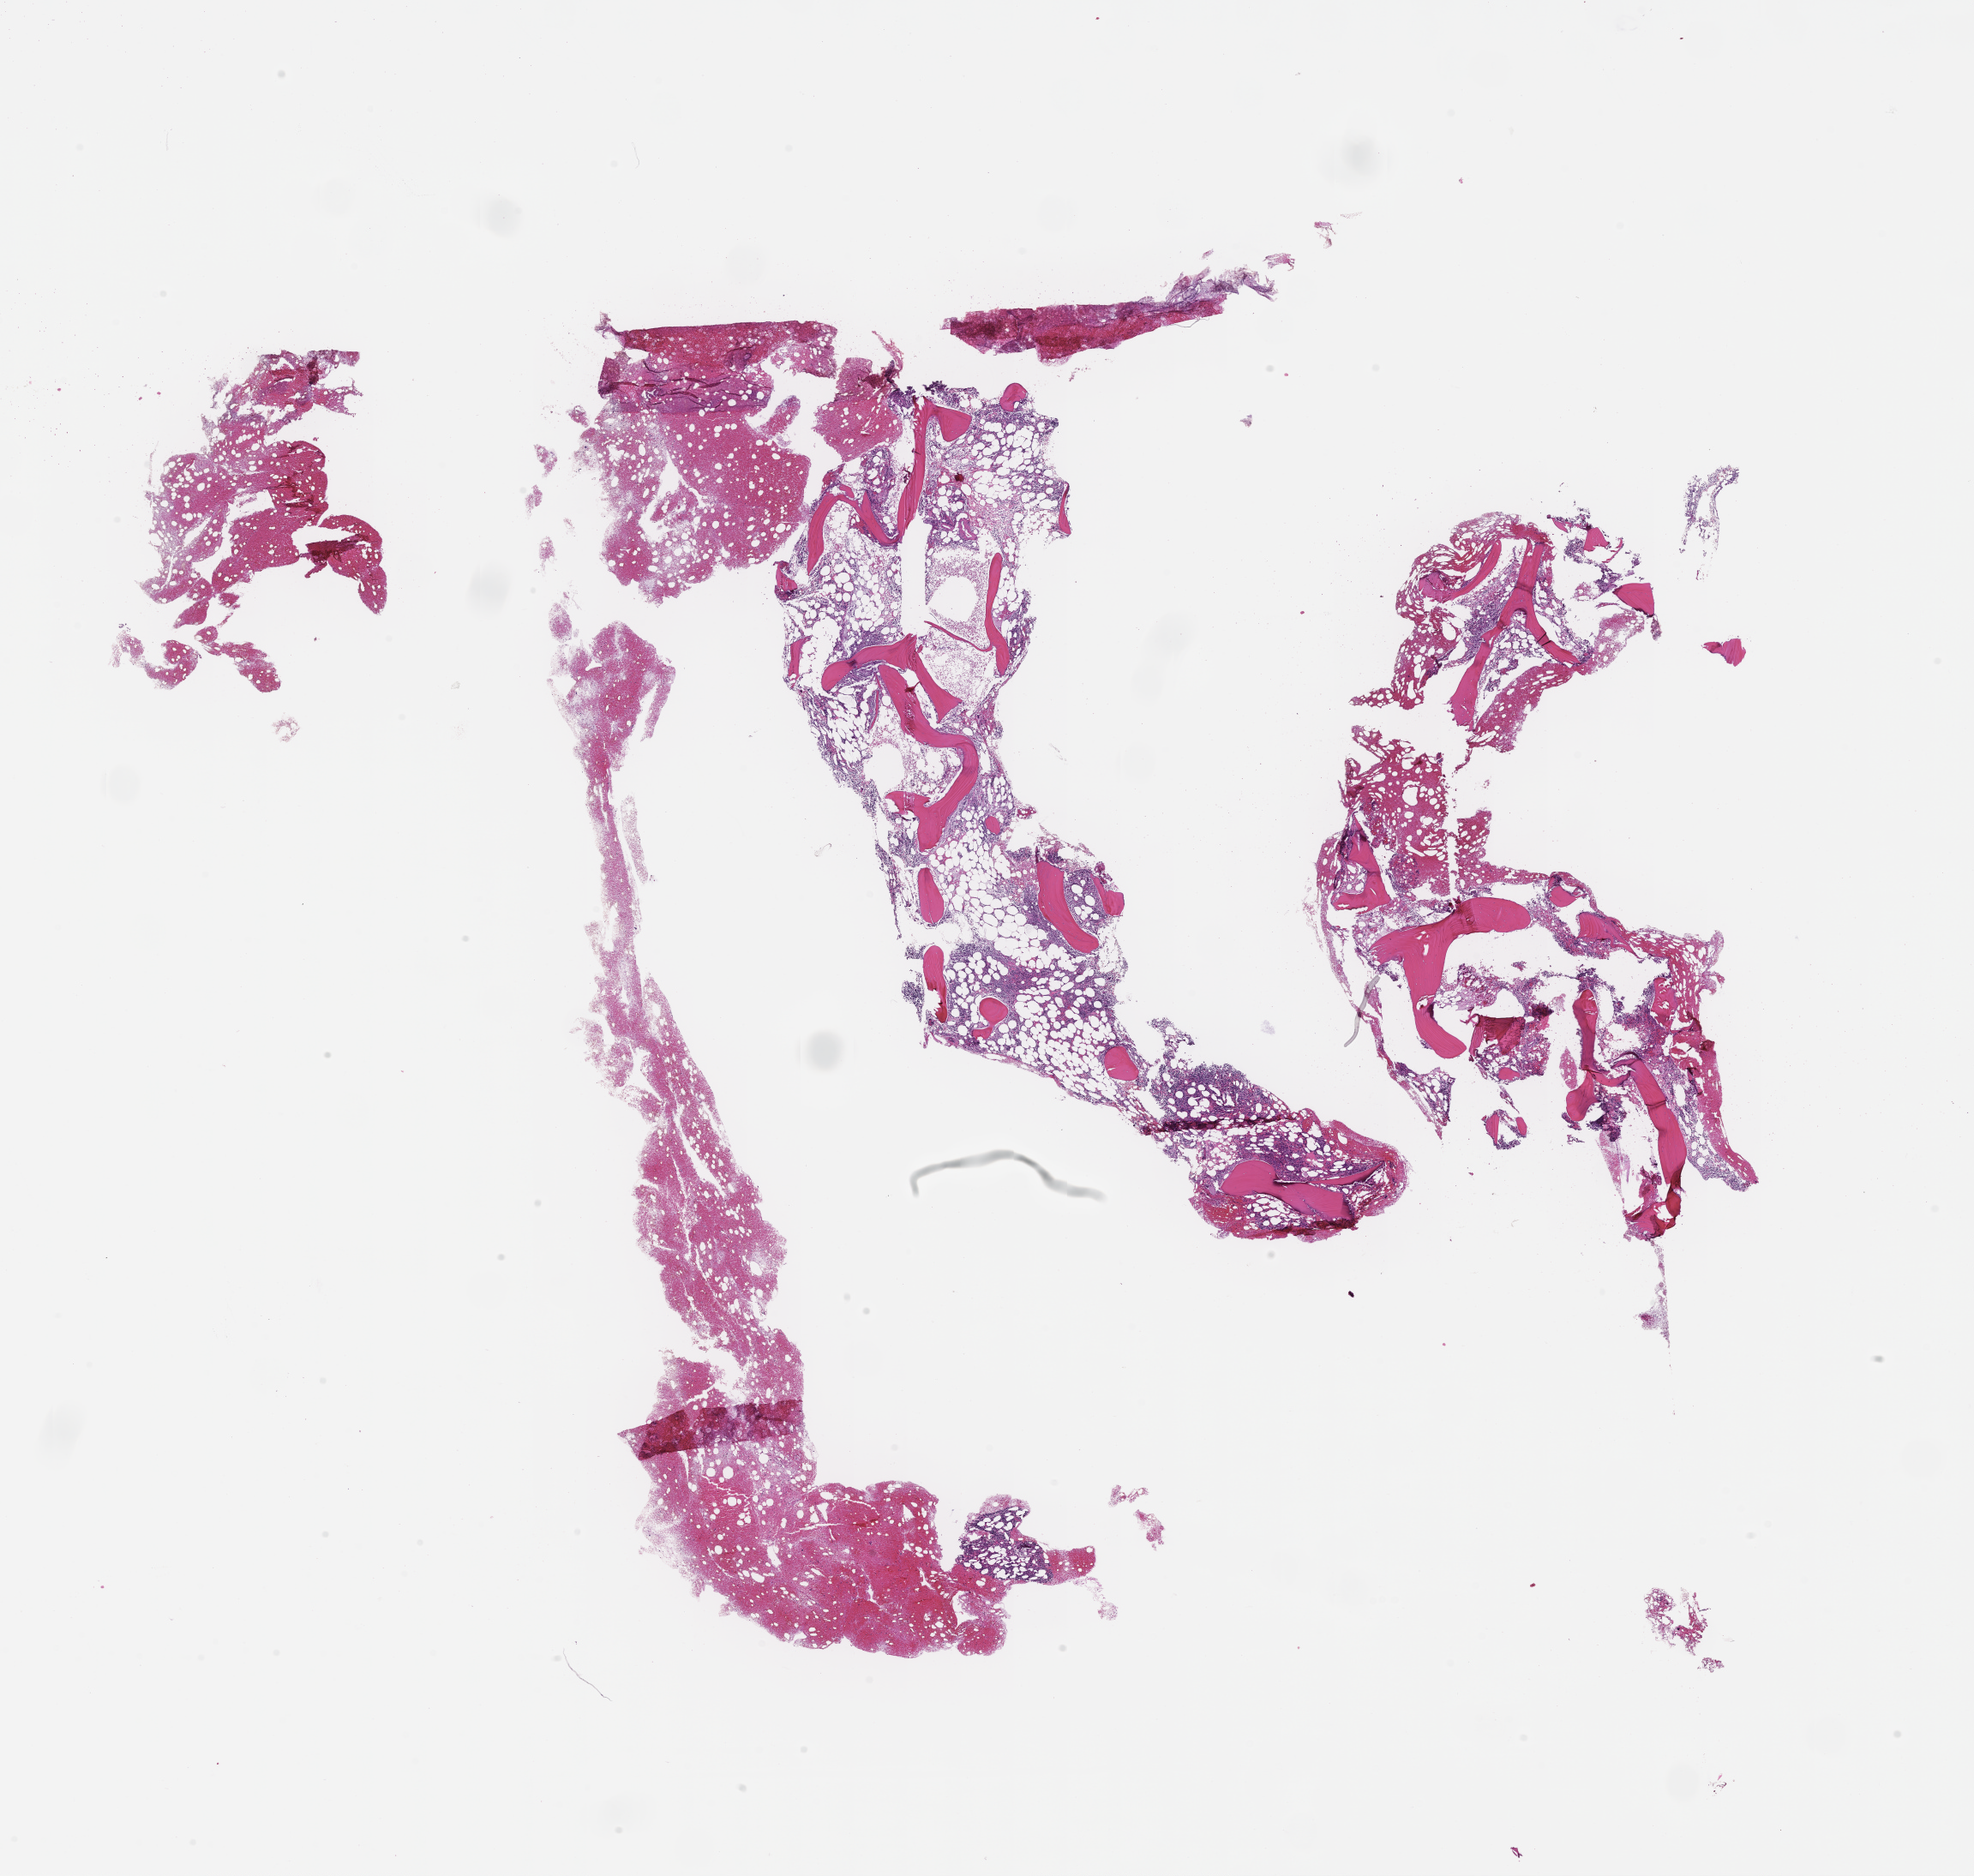
Digitized hematoxylin and eosin (H&E)-stained section, whole scanned area (about 18.6 x 17.7 mm) shown as a low-resolution overview; FFPE section; site: bone marrow; collected at baseline (before treatment). Patient sex: male.
Patient diagnosis: Plasma Cell Myeloma.